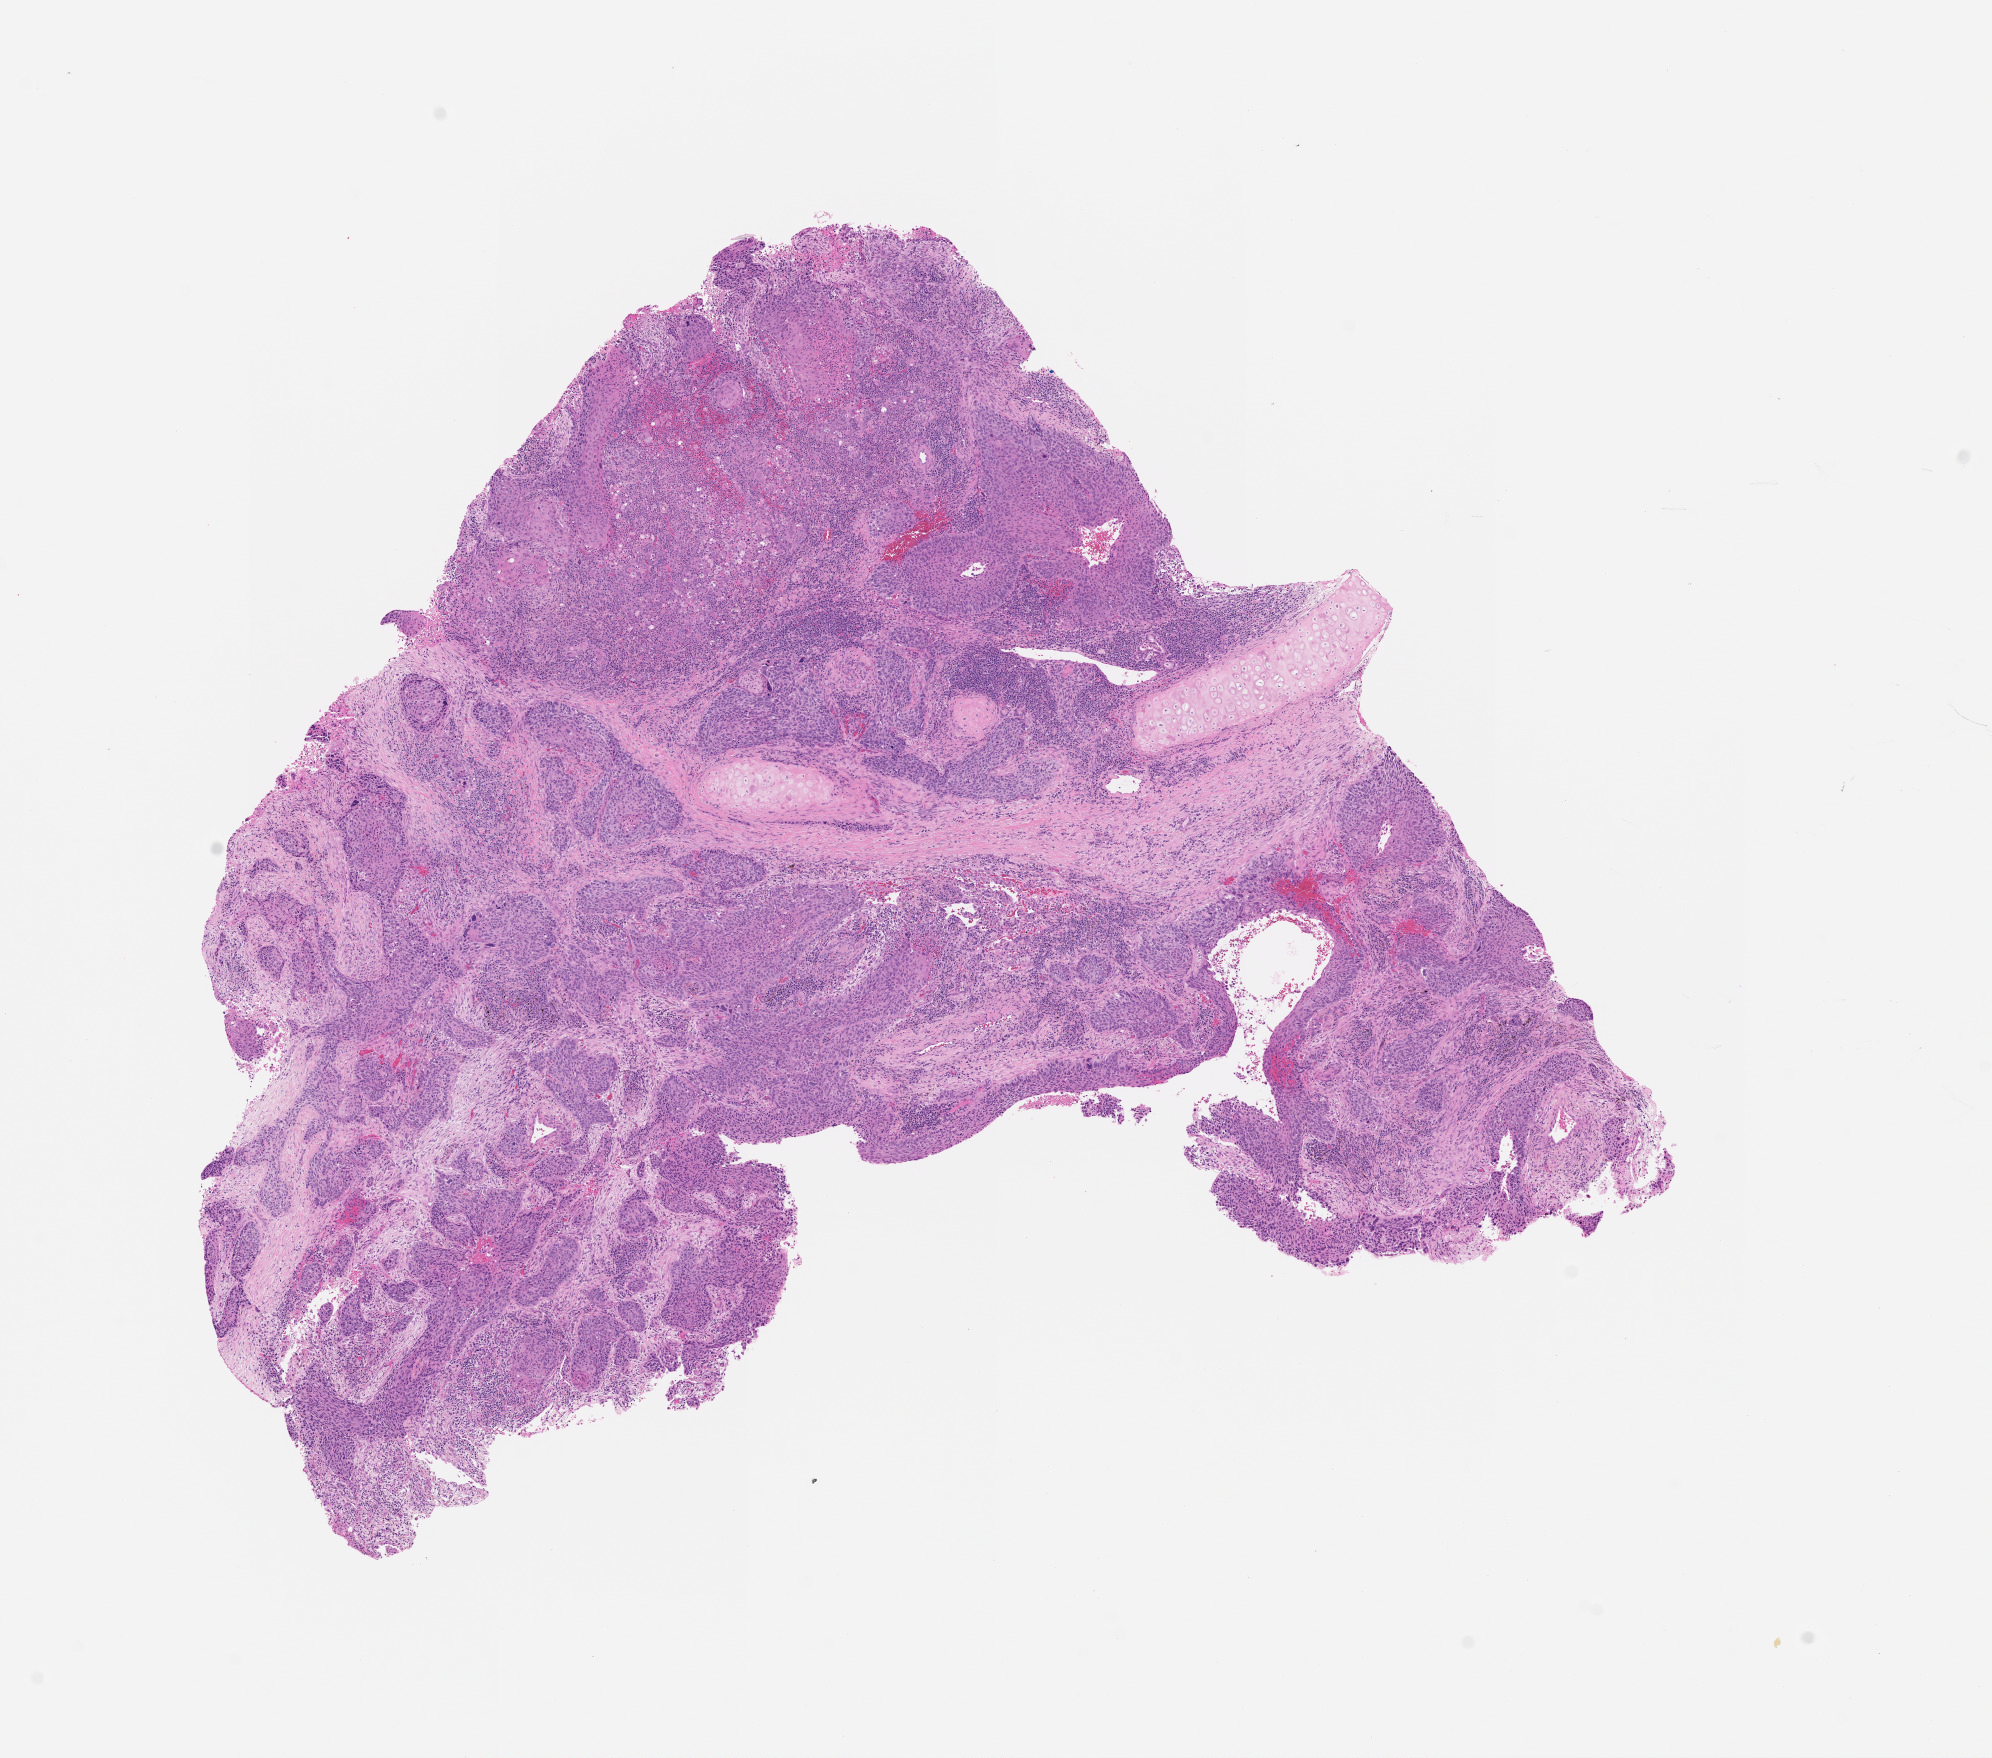
Digitized H&E tissue section (whole slide), whole scanned area (about 8.0 x 7.1 mm) shown as a low-resolution overview, tumour tissue sample, lung. 69-year-old male patient.
Patient diagnosis (cohort enrolment): squamous cell carcinoma (lung).